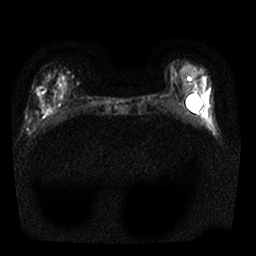
Breast MRI, one axial slice. Position 7 of 25 along the scan axis. Diffusion-weighted series; image 2 of 4 stored at this slice position (different b-values; order by instance number). 1.5 T. 4 mm slice thickness. 256 × 256 image matrix. Female patient.
Structures marked on this image (manually delineated by an expert):
- tumour on diffusion-weighted imaging: bounding box <36,87,45,96> (left, top, right, bottom; pixels)